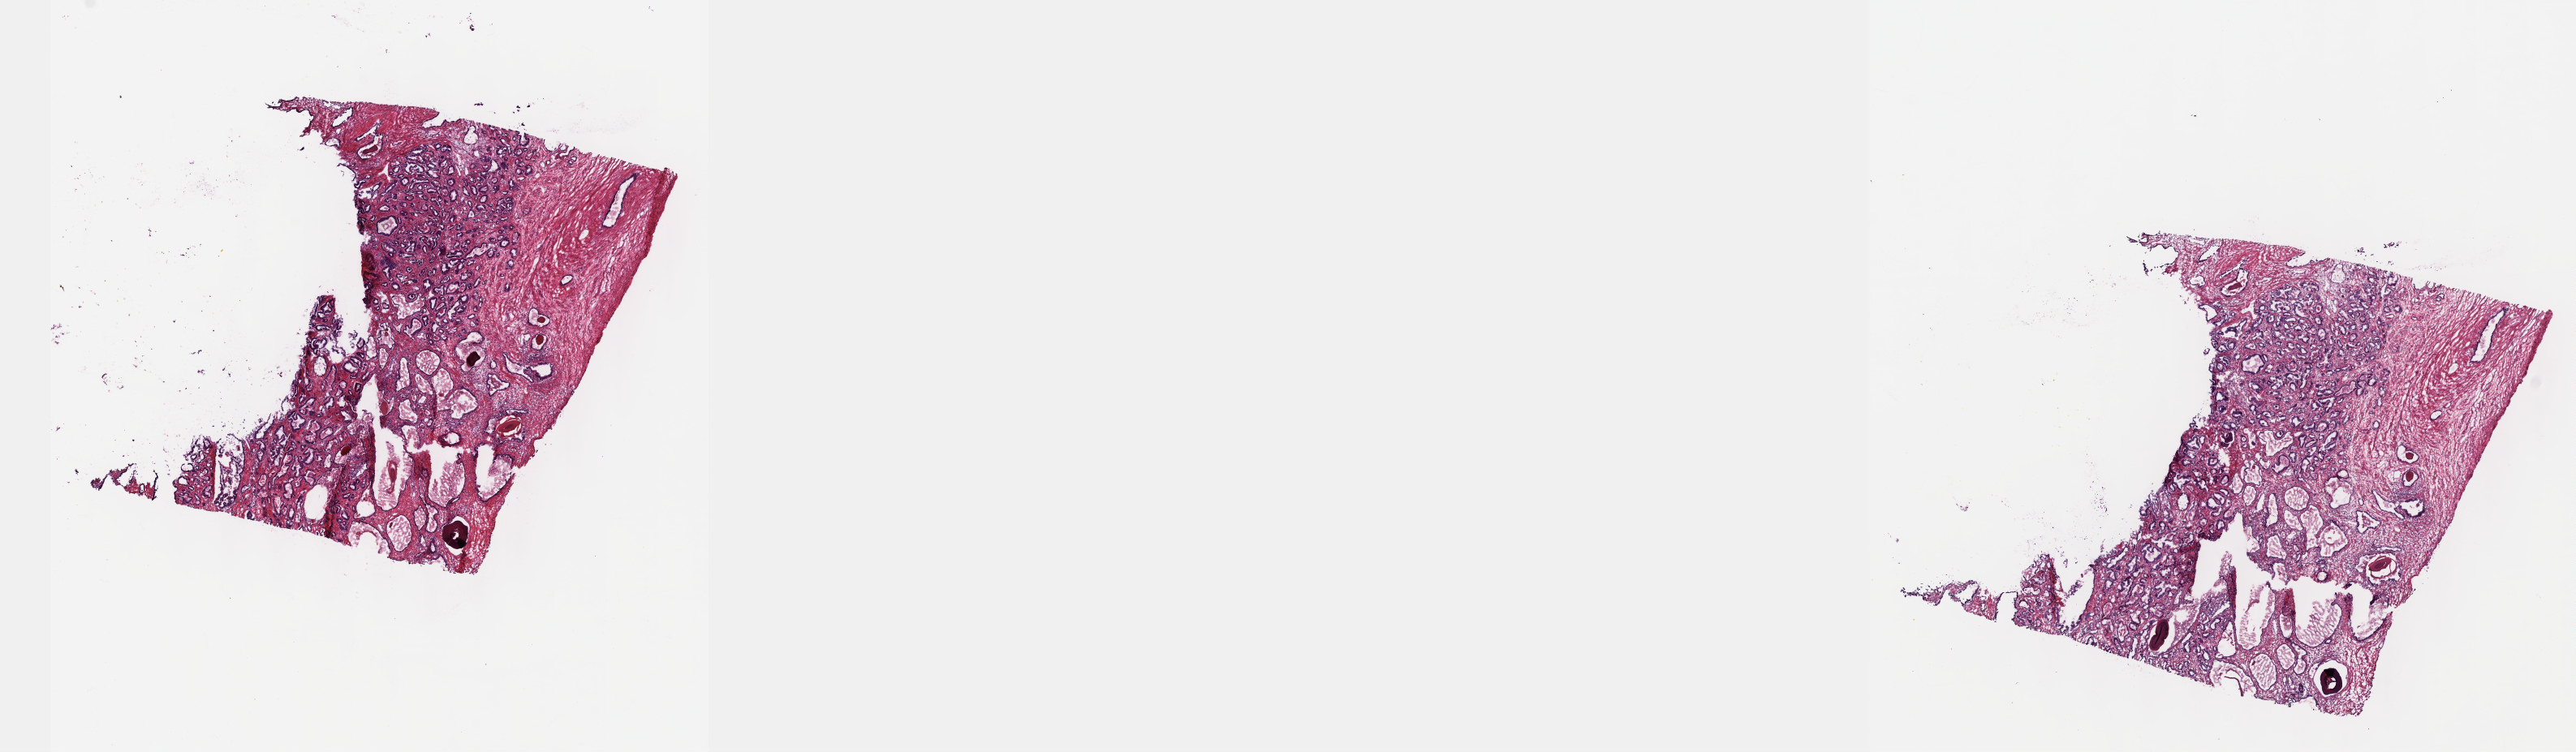
Whole-slide histology image, Hematoxylin and eosin (H&E) stained — a low-resolution overview of the entire scanned area, about 25.7 x 7.5 mm (slide scanned at 40x); frozen section; primary tumour sample from the prostate. Male, age 67 years at initial diagnosis. Gleason score: 7 (3+4). Composition of this section per pathologist review: tumour cells 60%, tumour nuclei 60%, normal cells 20%, stromal cells 20%, necrosis 0%. Inflammatory infiltration, as recorded: lymphocyte infiltration 2%, monocyte infiltration 0%, neutrophil infiltration 0%.
Lymph nodes positive (case pathology): 0 of 19 examined. Histologic diagnosis: Adenocarcinoma, NOS.